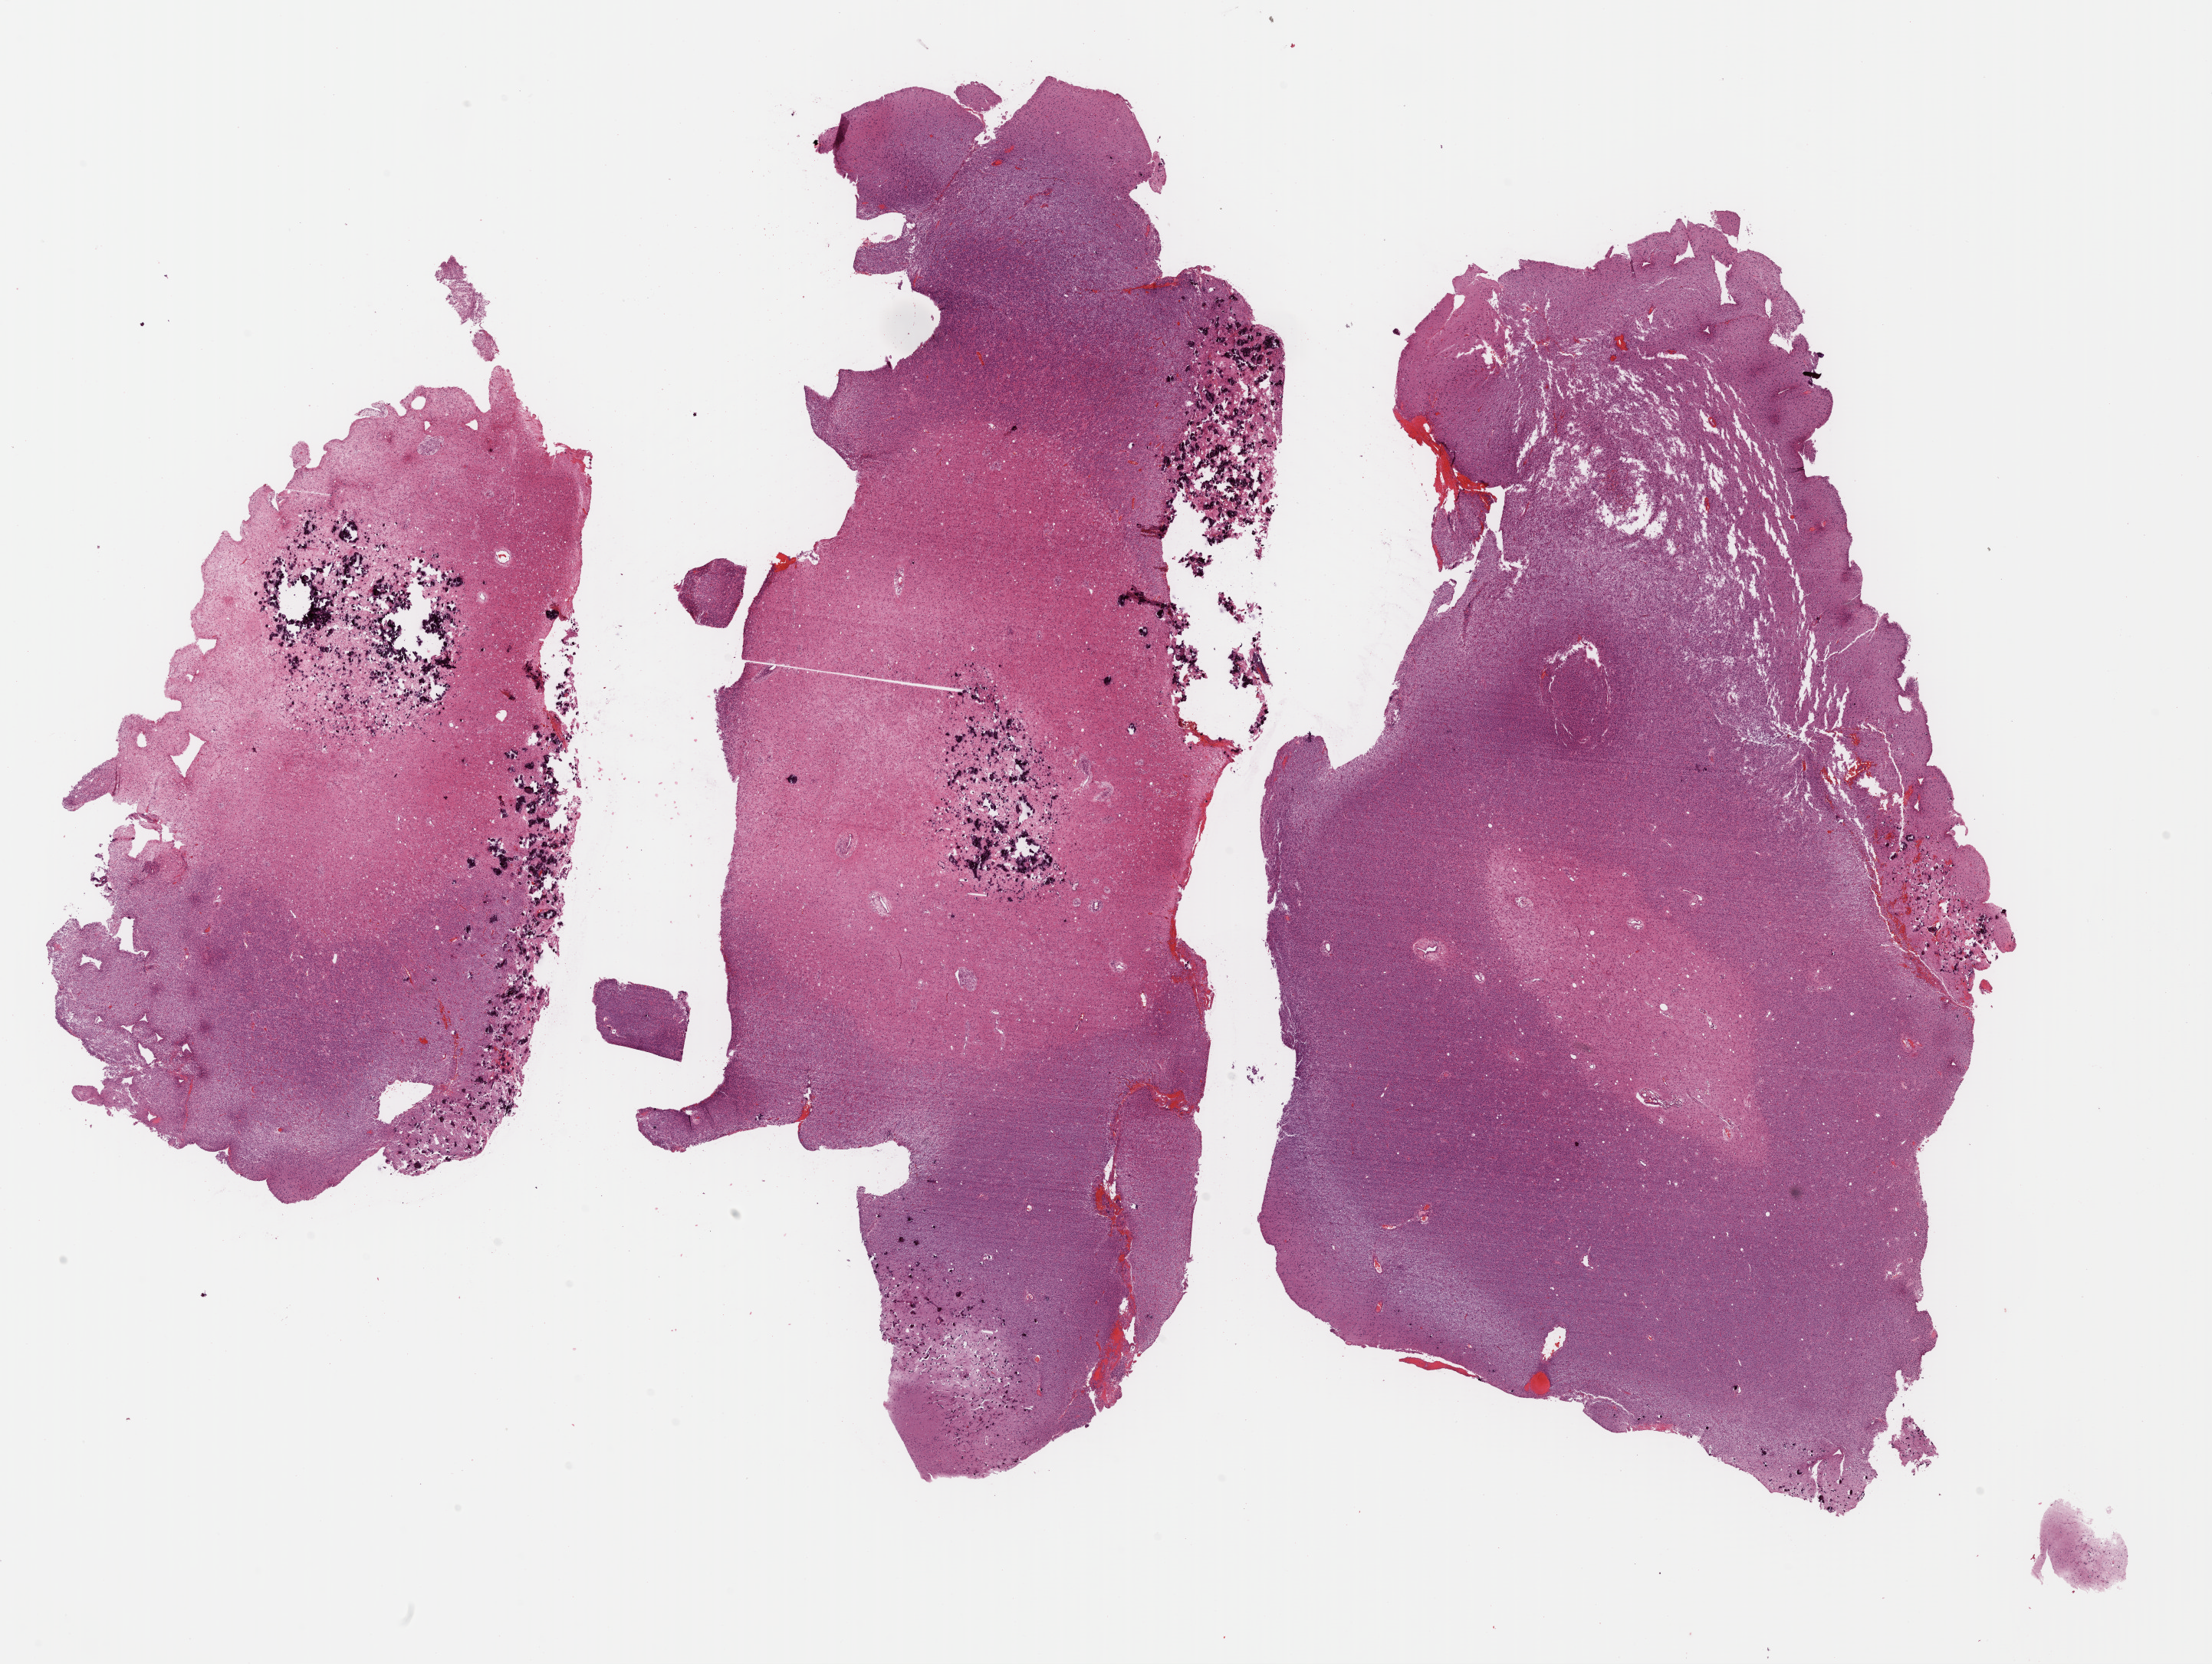
Digitized Hematoxylin and eosin (H&E) stained tissue section (whole slide), whole scanned area (about 22.7 x 17.1 mm, slide scanned at 40x) shown as a low-resolution overview; formalin-fixed paraffin-embedded (FFPE) diagnostic section; brain, primary tumour sample. Male patient; age at initial diagnosis 30 years. Histologic grade: G3 (poorly differentiated).
Laterality: right. Pathologic diagnosis: Oligodendroglioma, anaplastic (cerebrum).